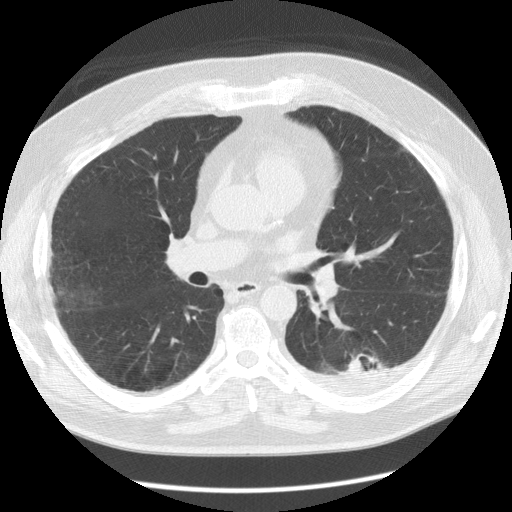
Low-dose screening chest CT, one axial slice; position 71 of 126 along the scan axis; reconstruction kernel STANDARD; 120 kVp; lung window (W 1500 / L -600 HU); 2.5 mm slice thickness; 512 × 512 image matrix, field of view 370 × 370 mm.
Outlined on this slice (expert manual segmentation):
- lesion 1 (tumor, lower lobe of left lung): bounding box [x1, y1, x2, y2] px = [342, 353, 382, 374]